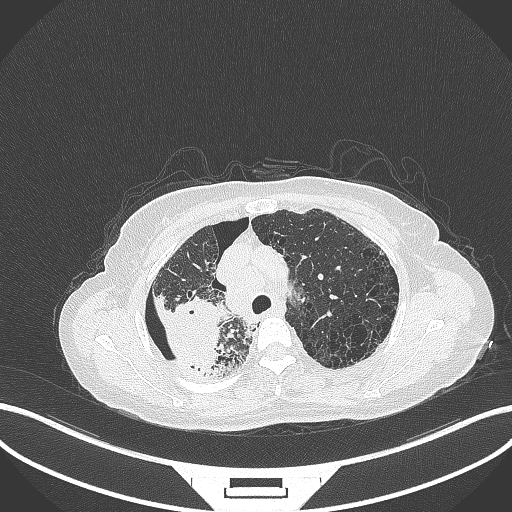
Chest CT, one axial slice. Position 266 of 408 along the scan axis. Reconstruction kernel B70f. Lung window (W 1500 / L -600 HU). 1 mm slice thickness. 512 × 512 image matrix. Female patient, age 64 years. Case-level facts recorded for this patient, not image findings: clinical TNM (as recorded): T3 N3 M0.
Outlined on this slice (bounding box drawn by a radiologist):
- lung tumour (recorded histology: squamous cell carcinoma): bounding box [x1, y1, x2, y2] px = [152, 287, 222, 375]